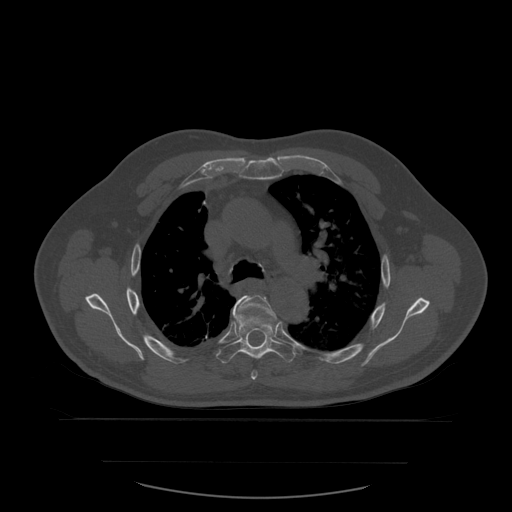
CT including the spine, one axial slice. Slice 411 of 590 in the series (ordered by position). Bone window (W 1800 / L 400 HU). 1.25 mm slice thickness. 512 × 512 image matrix, field of view 479 × 479 mm. Patient age 71 years. From the clinical record (not read from this slice): primary cancer: lung.
Outlined on this slice (semi-automatic segmentation, software-assisted and operator-edited):
- T5 vertebra: box from (x=235, y=295) to (x=276, y=380) px
- T6 vertebra: (x=217, y=307)–(x=296, y=364)